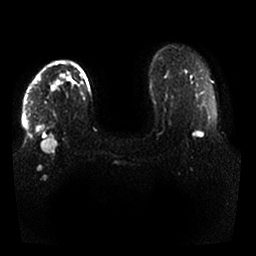
Breast MRI, one axial slice; slice 23 of 25 in the series (ordered by position); diffusion-weighted series; image 2 of 4 stored at this slice position (different b-values; order by instance number); 1.5 T; 256 × 256 image matrix, field of view 350 × 350 mm. Female patient.
Outlined on this slice (expert manual segmentation):
- tumour on diffusion-weighted imaging: bounding box [x1, y1, x2, y2] px = [41, 73, 70, 153]